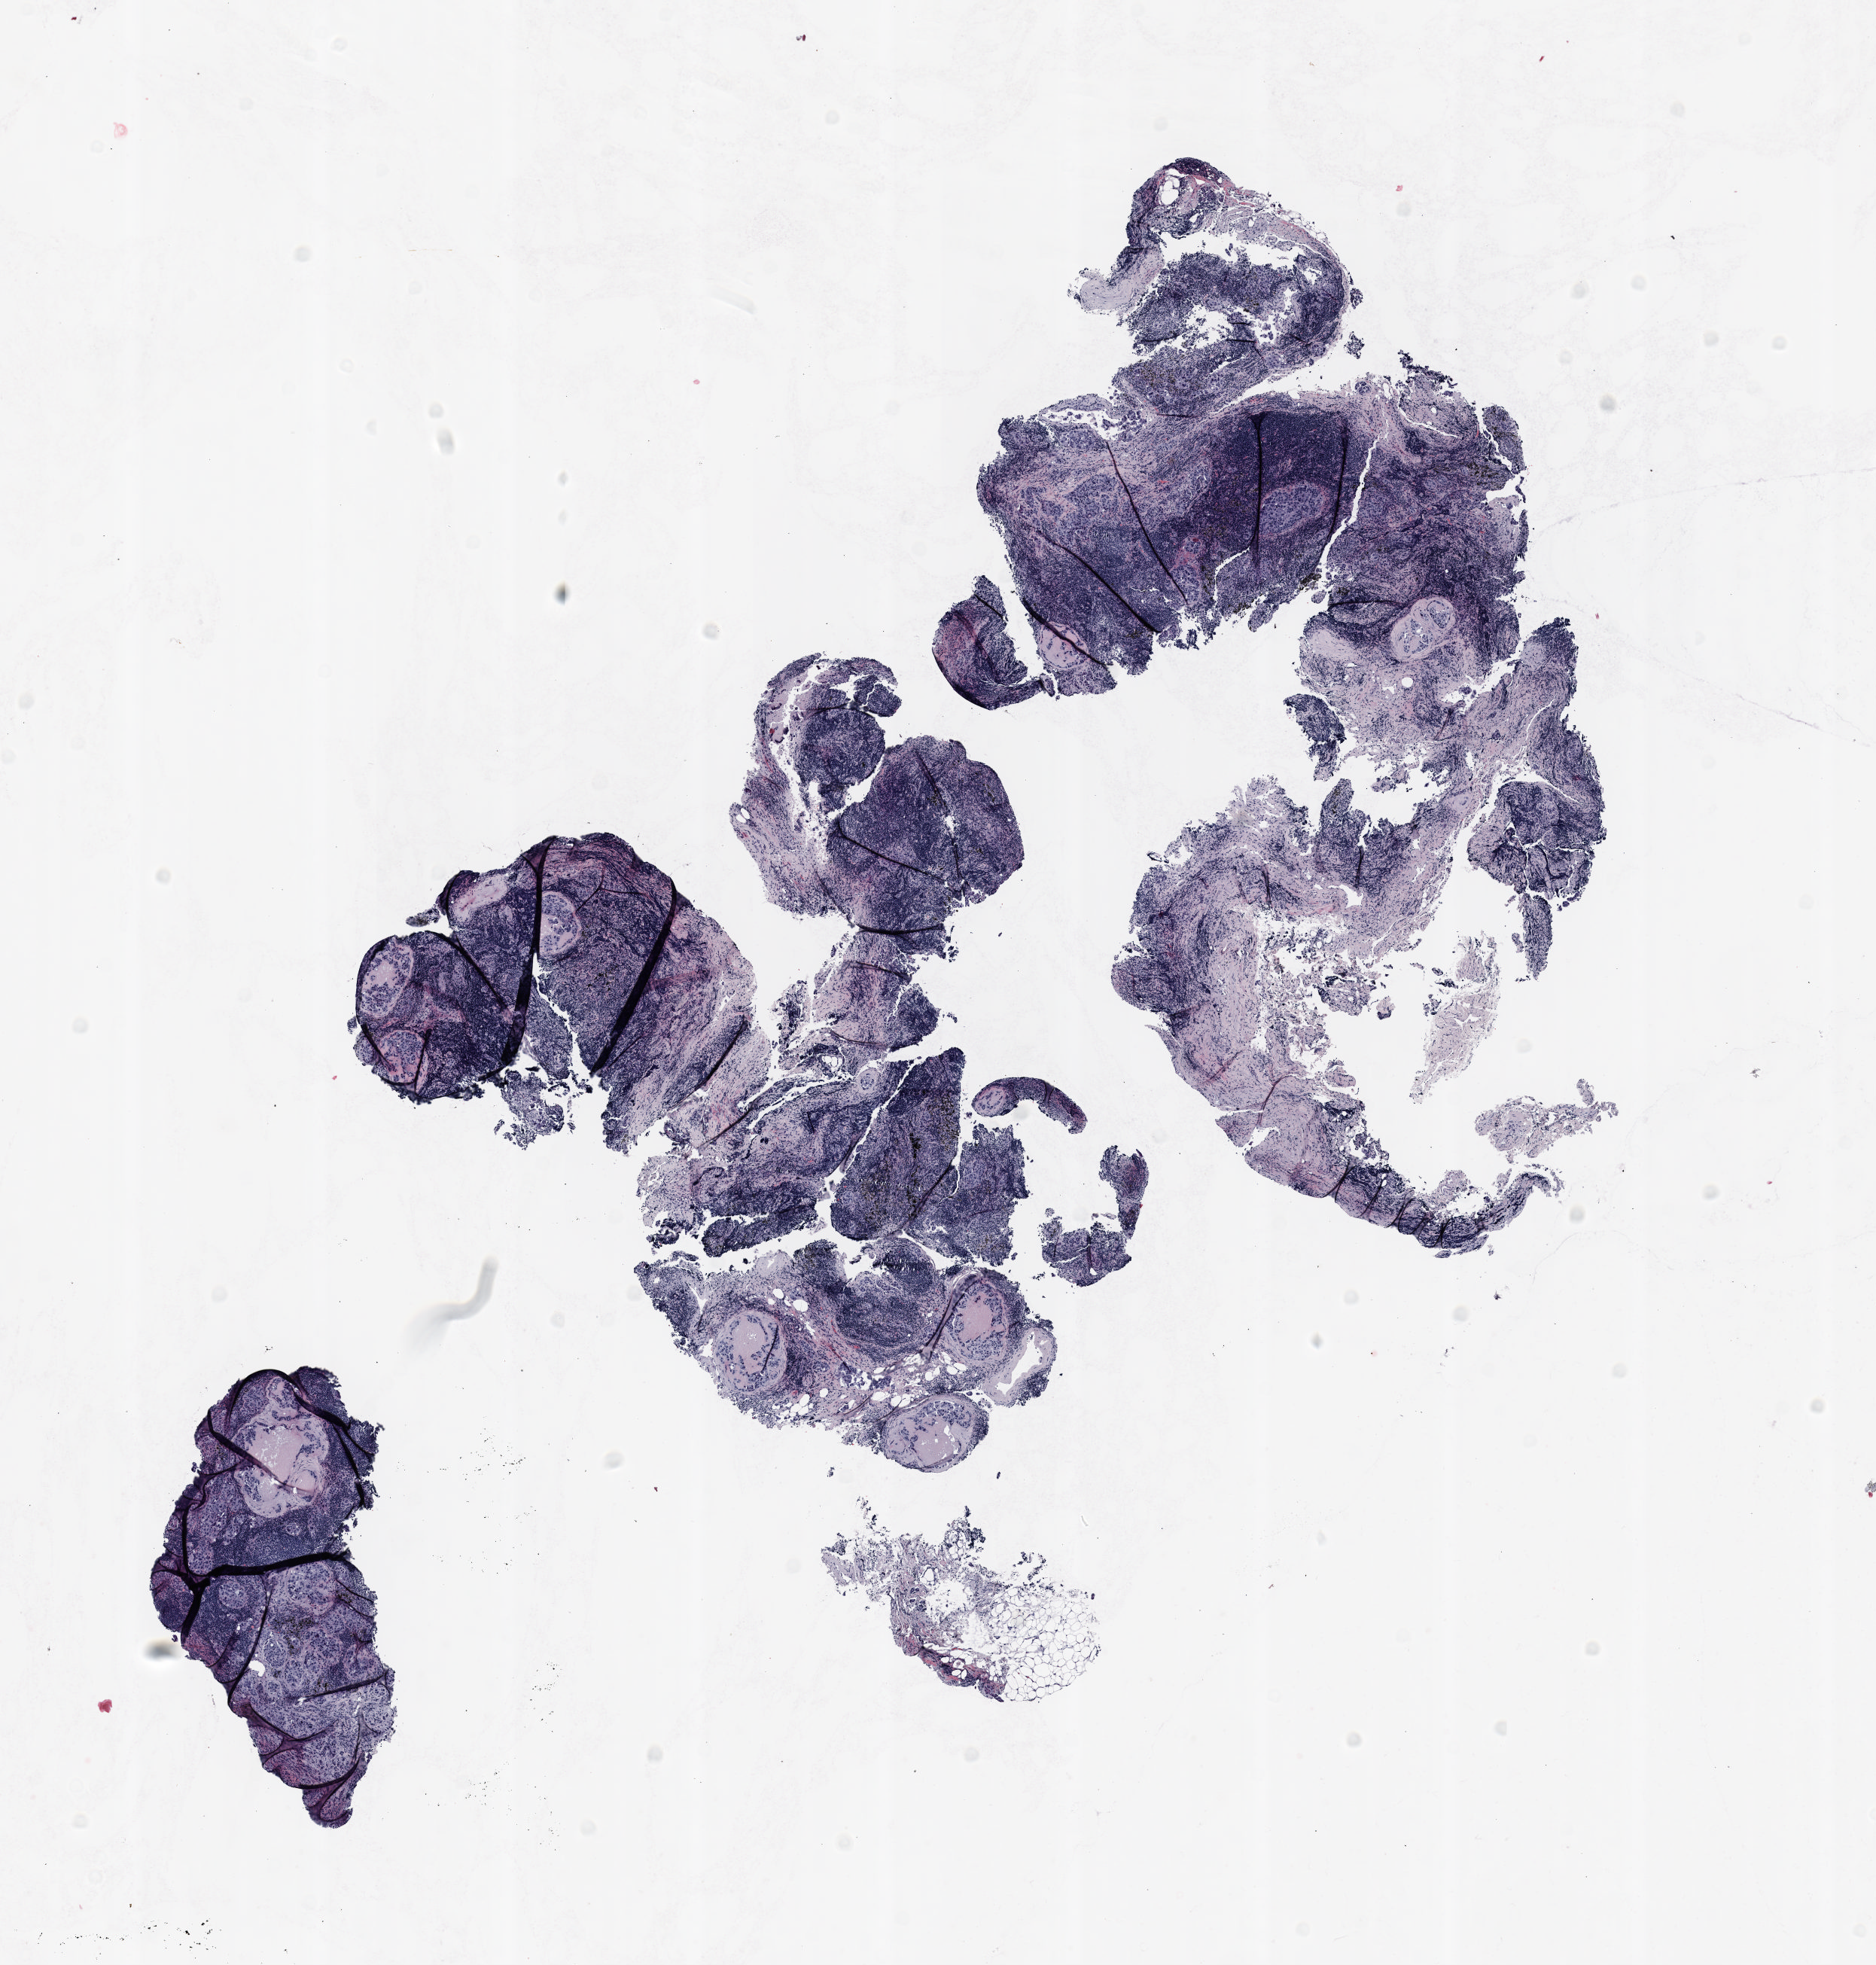
Whole-slide histology image, H&E-stained — low-resolution overview of the scanned area, about 10.0 x 10.5 mm (from a 20x scan); formalin-fixed paraffin-embedded (FFPE) section; lung tissue. Female, age 63 at enrolment. Current smoker at enrolment.
Participant's lung-cancer diagnosis: Papillary adenocarcinoma, NOS.